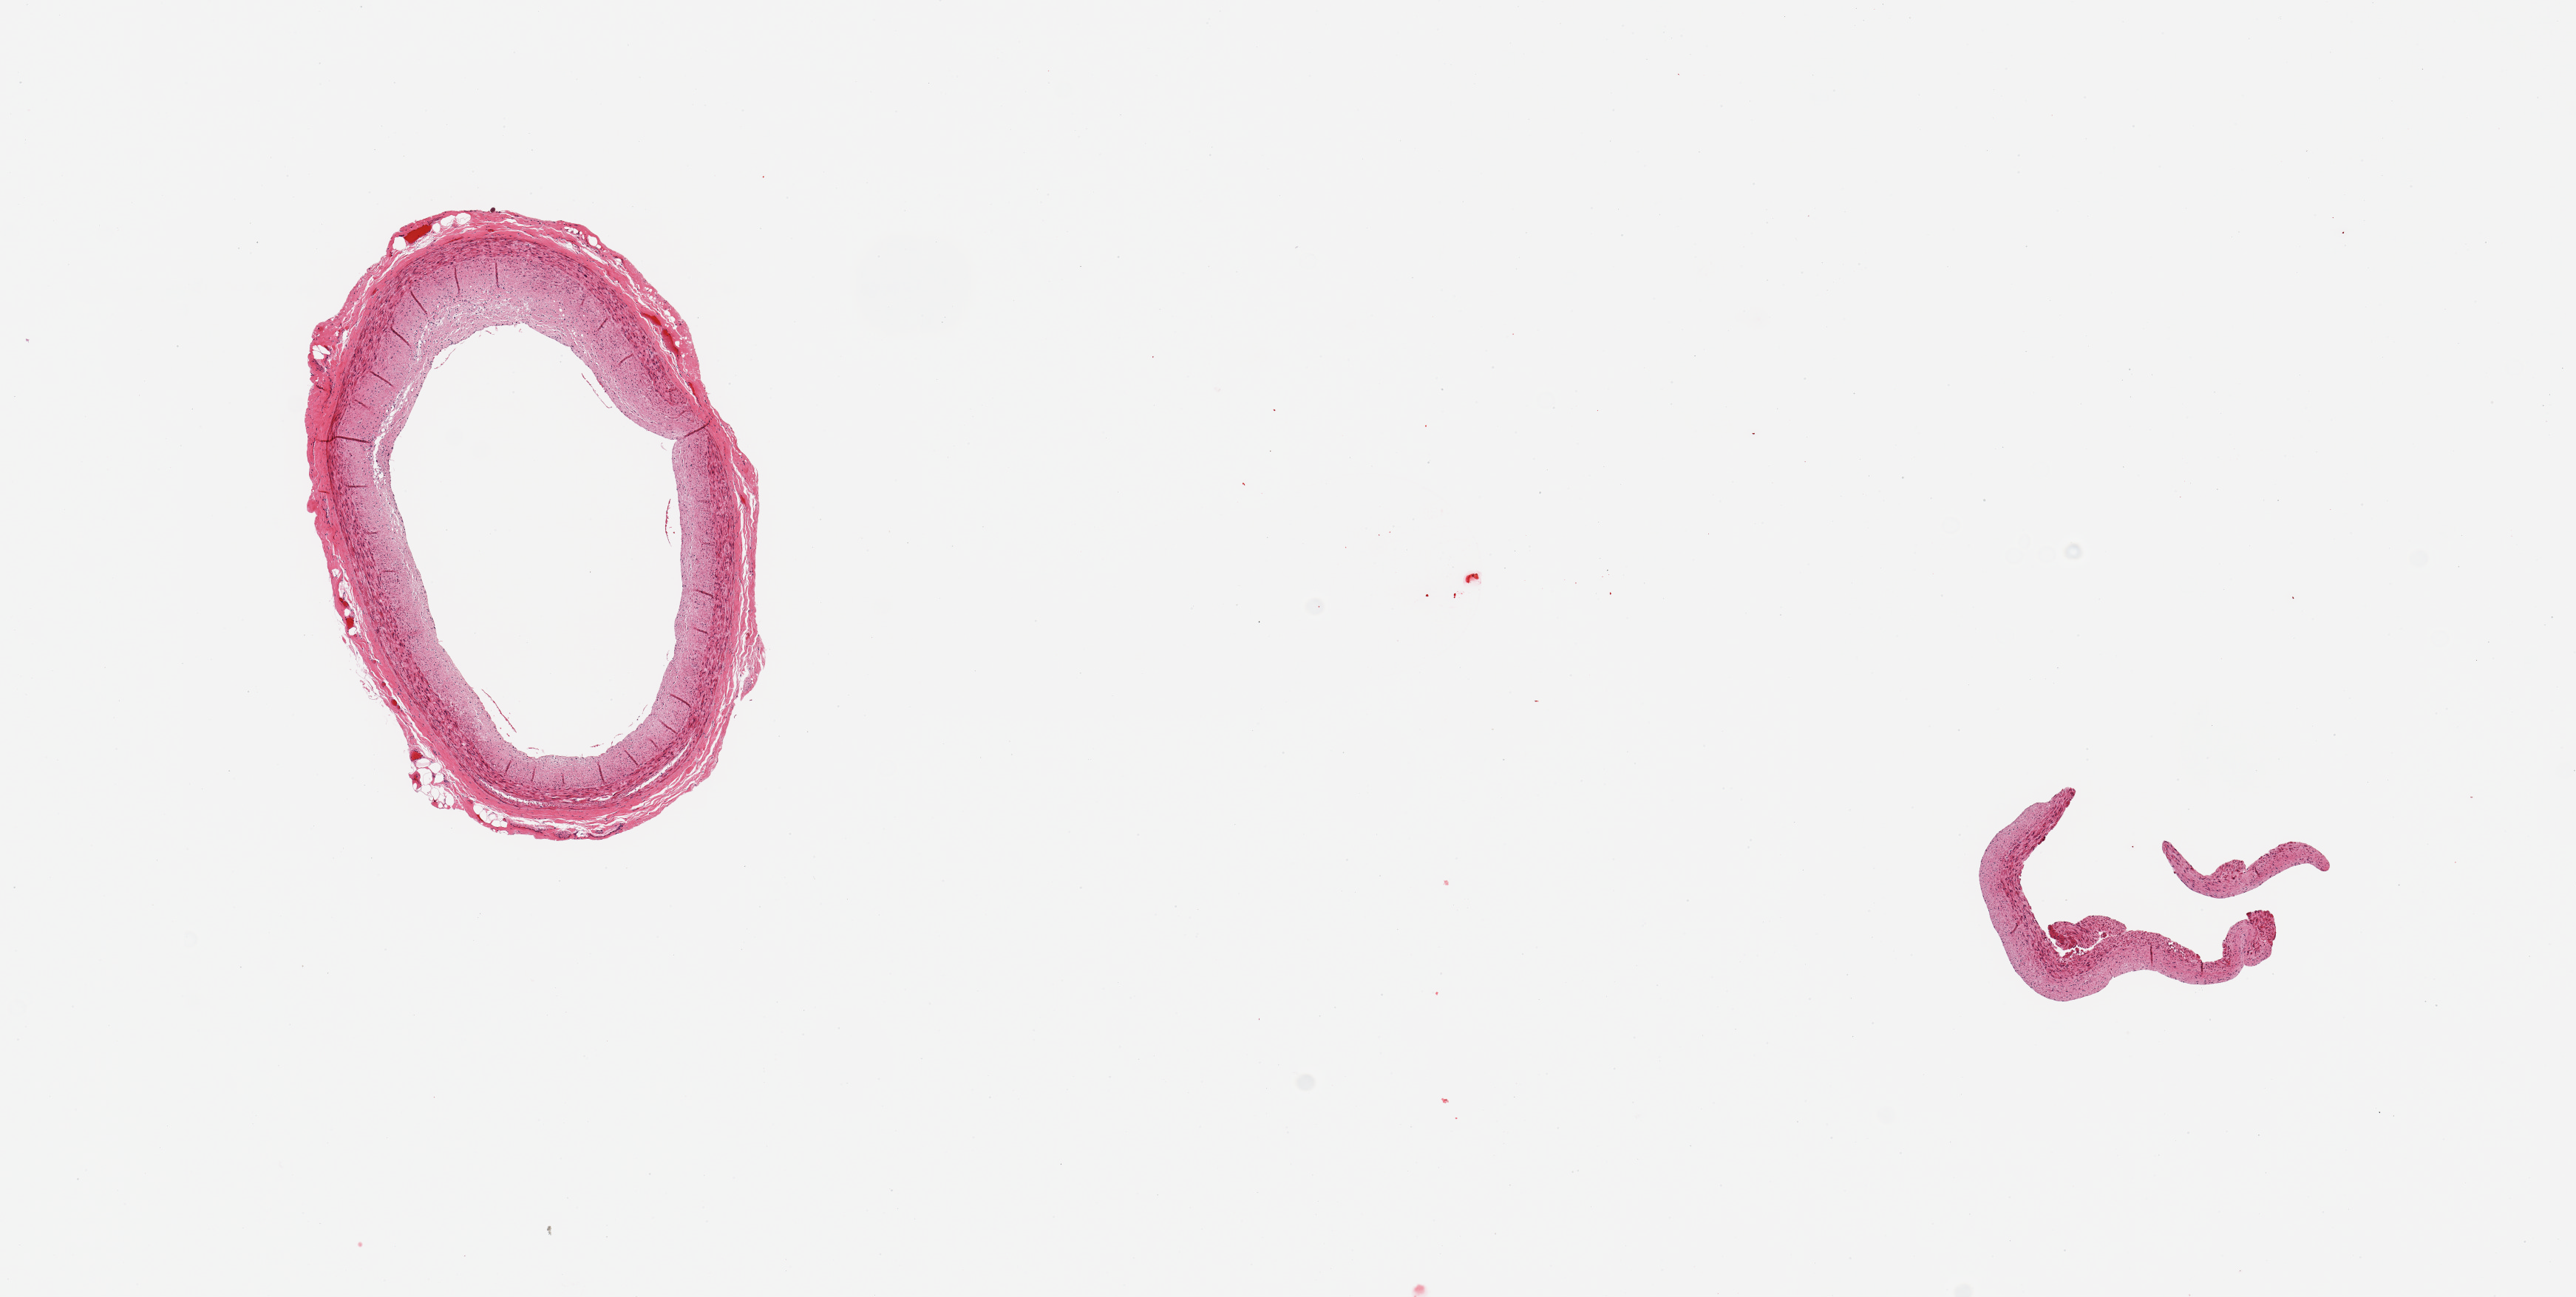
Digitized haematoxylin and eosin-stained section, brightfield, whole scanned area (about 13.8 x 6.9 mm, slide scanned at 20x) shown as a low-resolution overview; PAXgene-fixed paraffin-embedded (PFPE) section; section of coronary artery (target tissue); donor tissue sample. Male donor.
Pathologist's review note for this sample: 2 pieces; one piece with patent lumen and early intimal atheromatous plaque; other repersents scant framents of vessel wall.